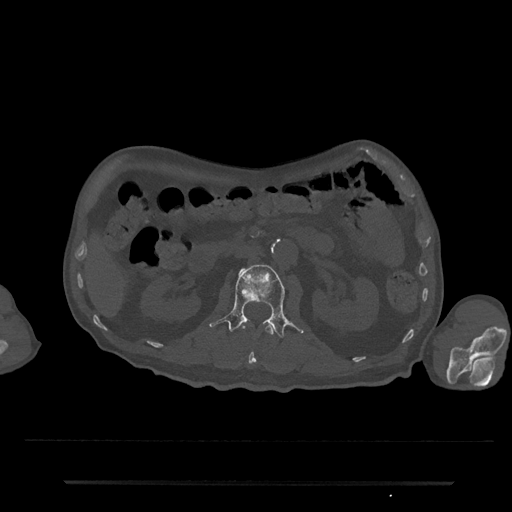
CT including the spine, one axial slice; position 79 of 797 along the scan axis; 120 kVp; bone window (W 1800 / L 400 HU); 0.5 mm slice thickness; 512 × 512 image matrix, field of view 427 × 427 mm. Male patient, age 74 years. From the clinical record (not read from this slice): primary cancer: prostate.
Structures marked on this image (semi-automatic segmentation, software-assisted and operator-edited):
- L1 vertebra: bounding box (x1, y1, x2, y2) in pixels: (241, 324, 274, 366)
- L2 vertebra: (209, 264, 303, 339)